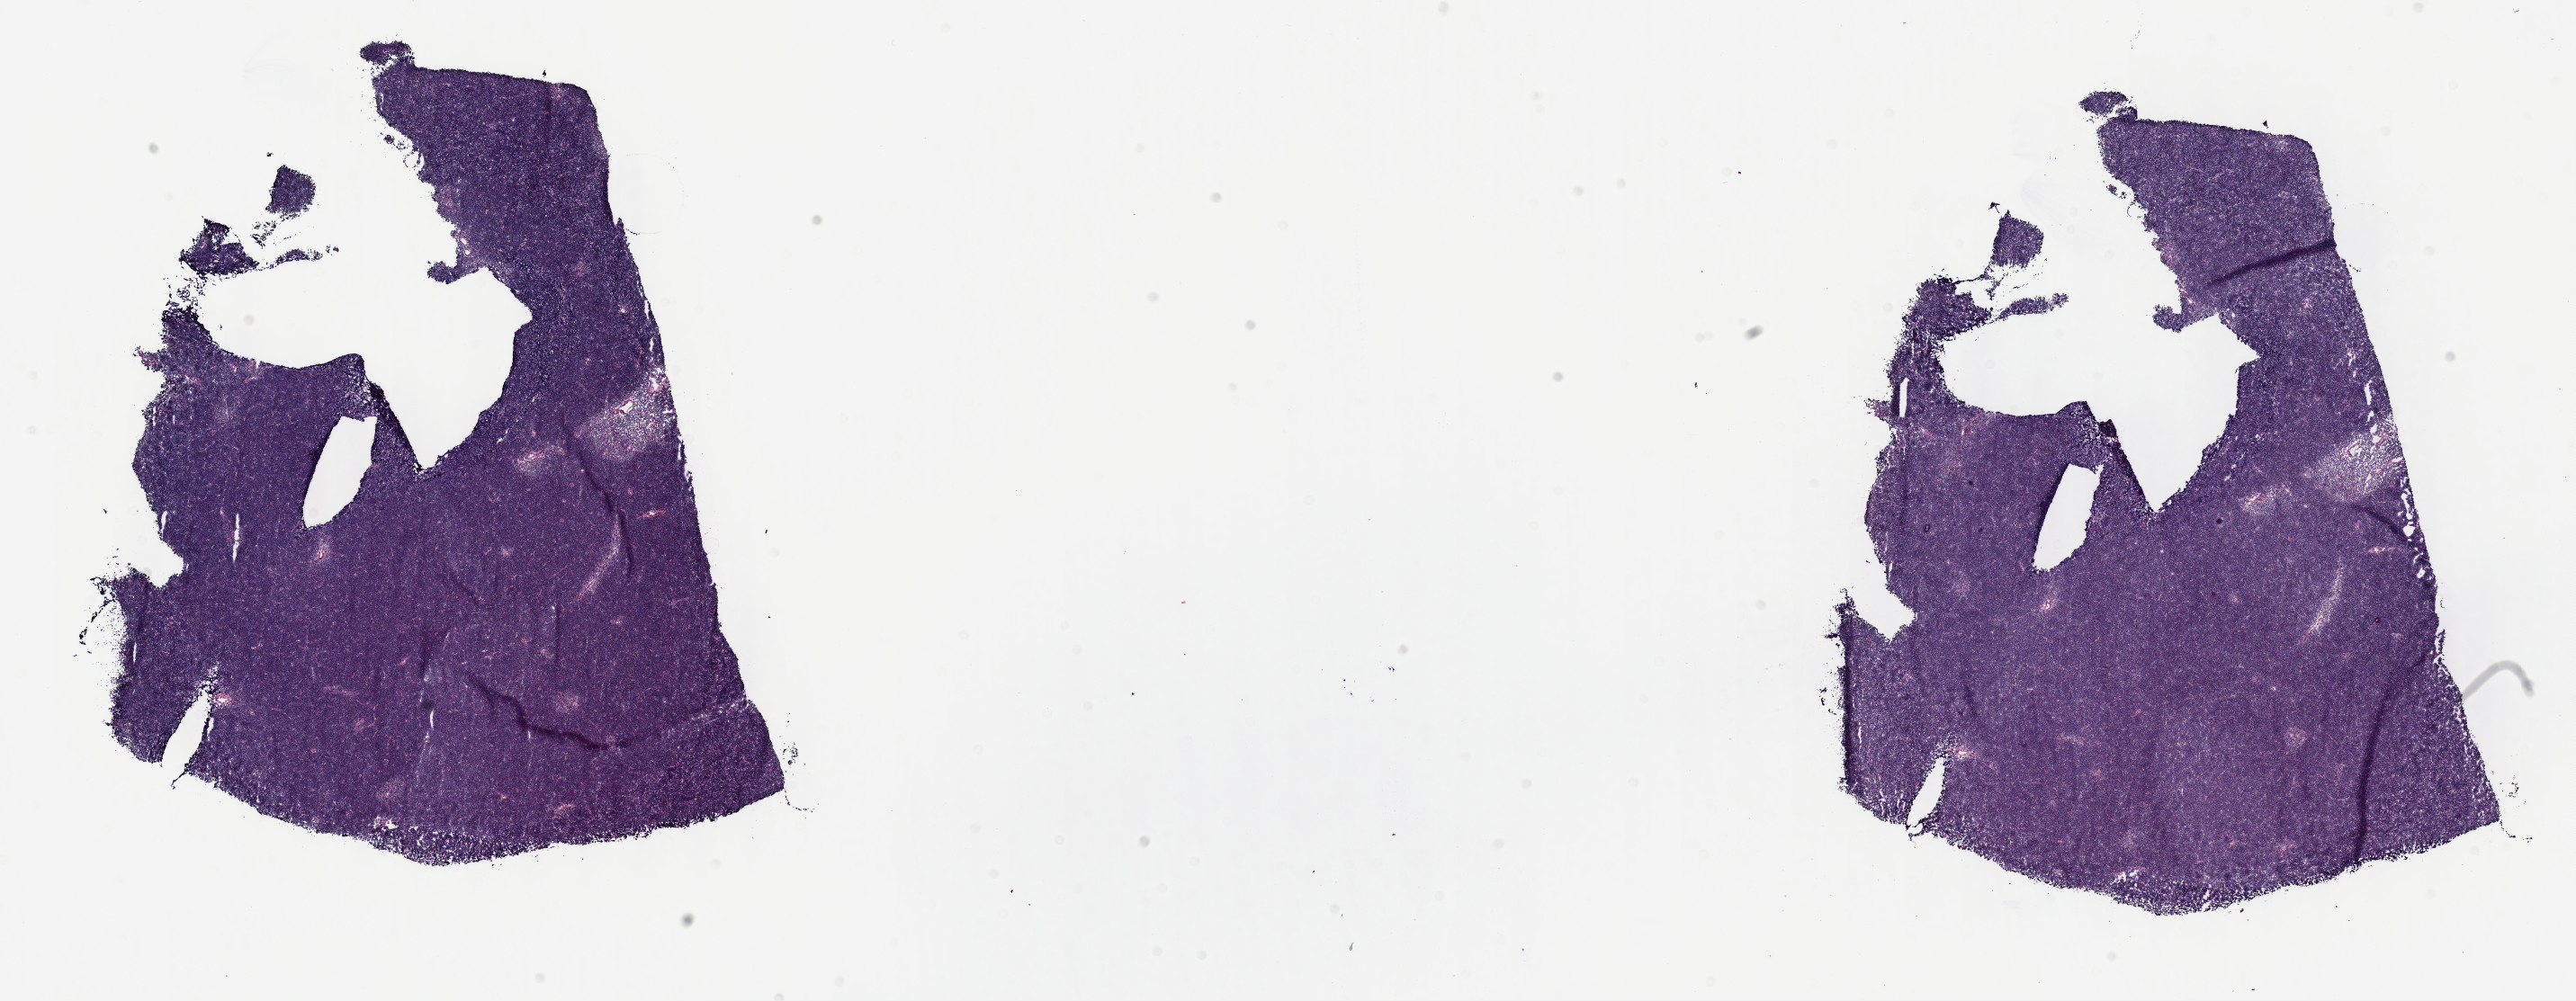
H&E whole-slide image — whole scanned area (about 23.2 x 9.0 mm, slide scanned at 40x) shown as a low-resolution overview; frozen section from the top of the tissue portion; primary tumour sample from the thymus. Female, age 55 years at initial diagnosis.
Histologic diagnosis: Thymoma, type B1, NOS.